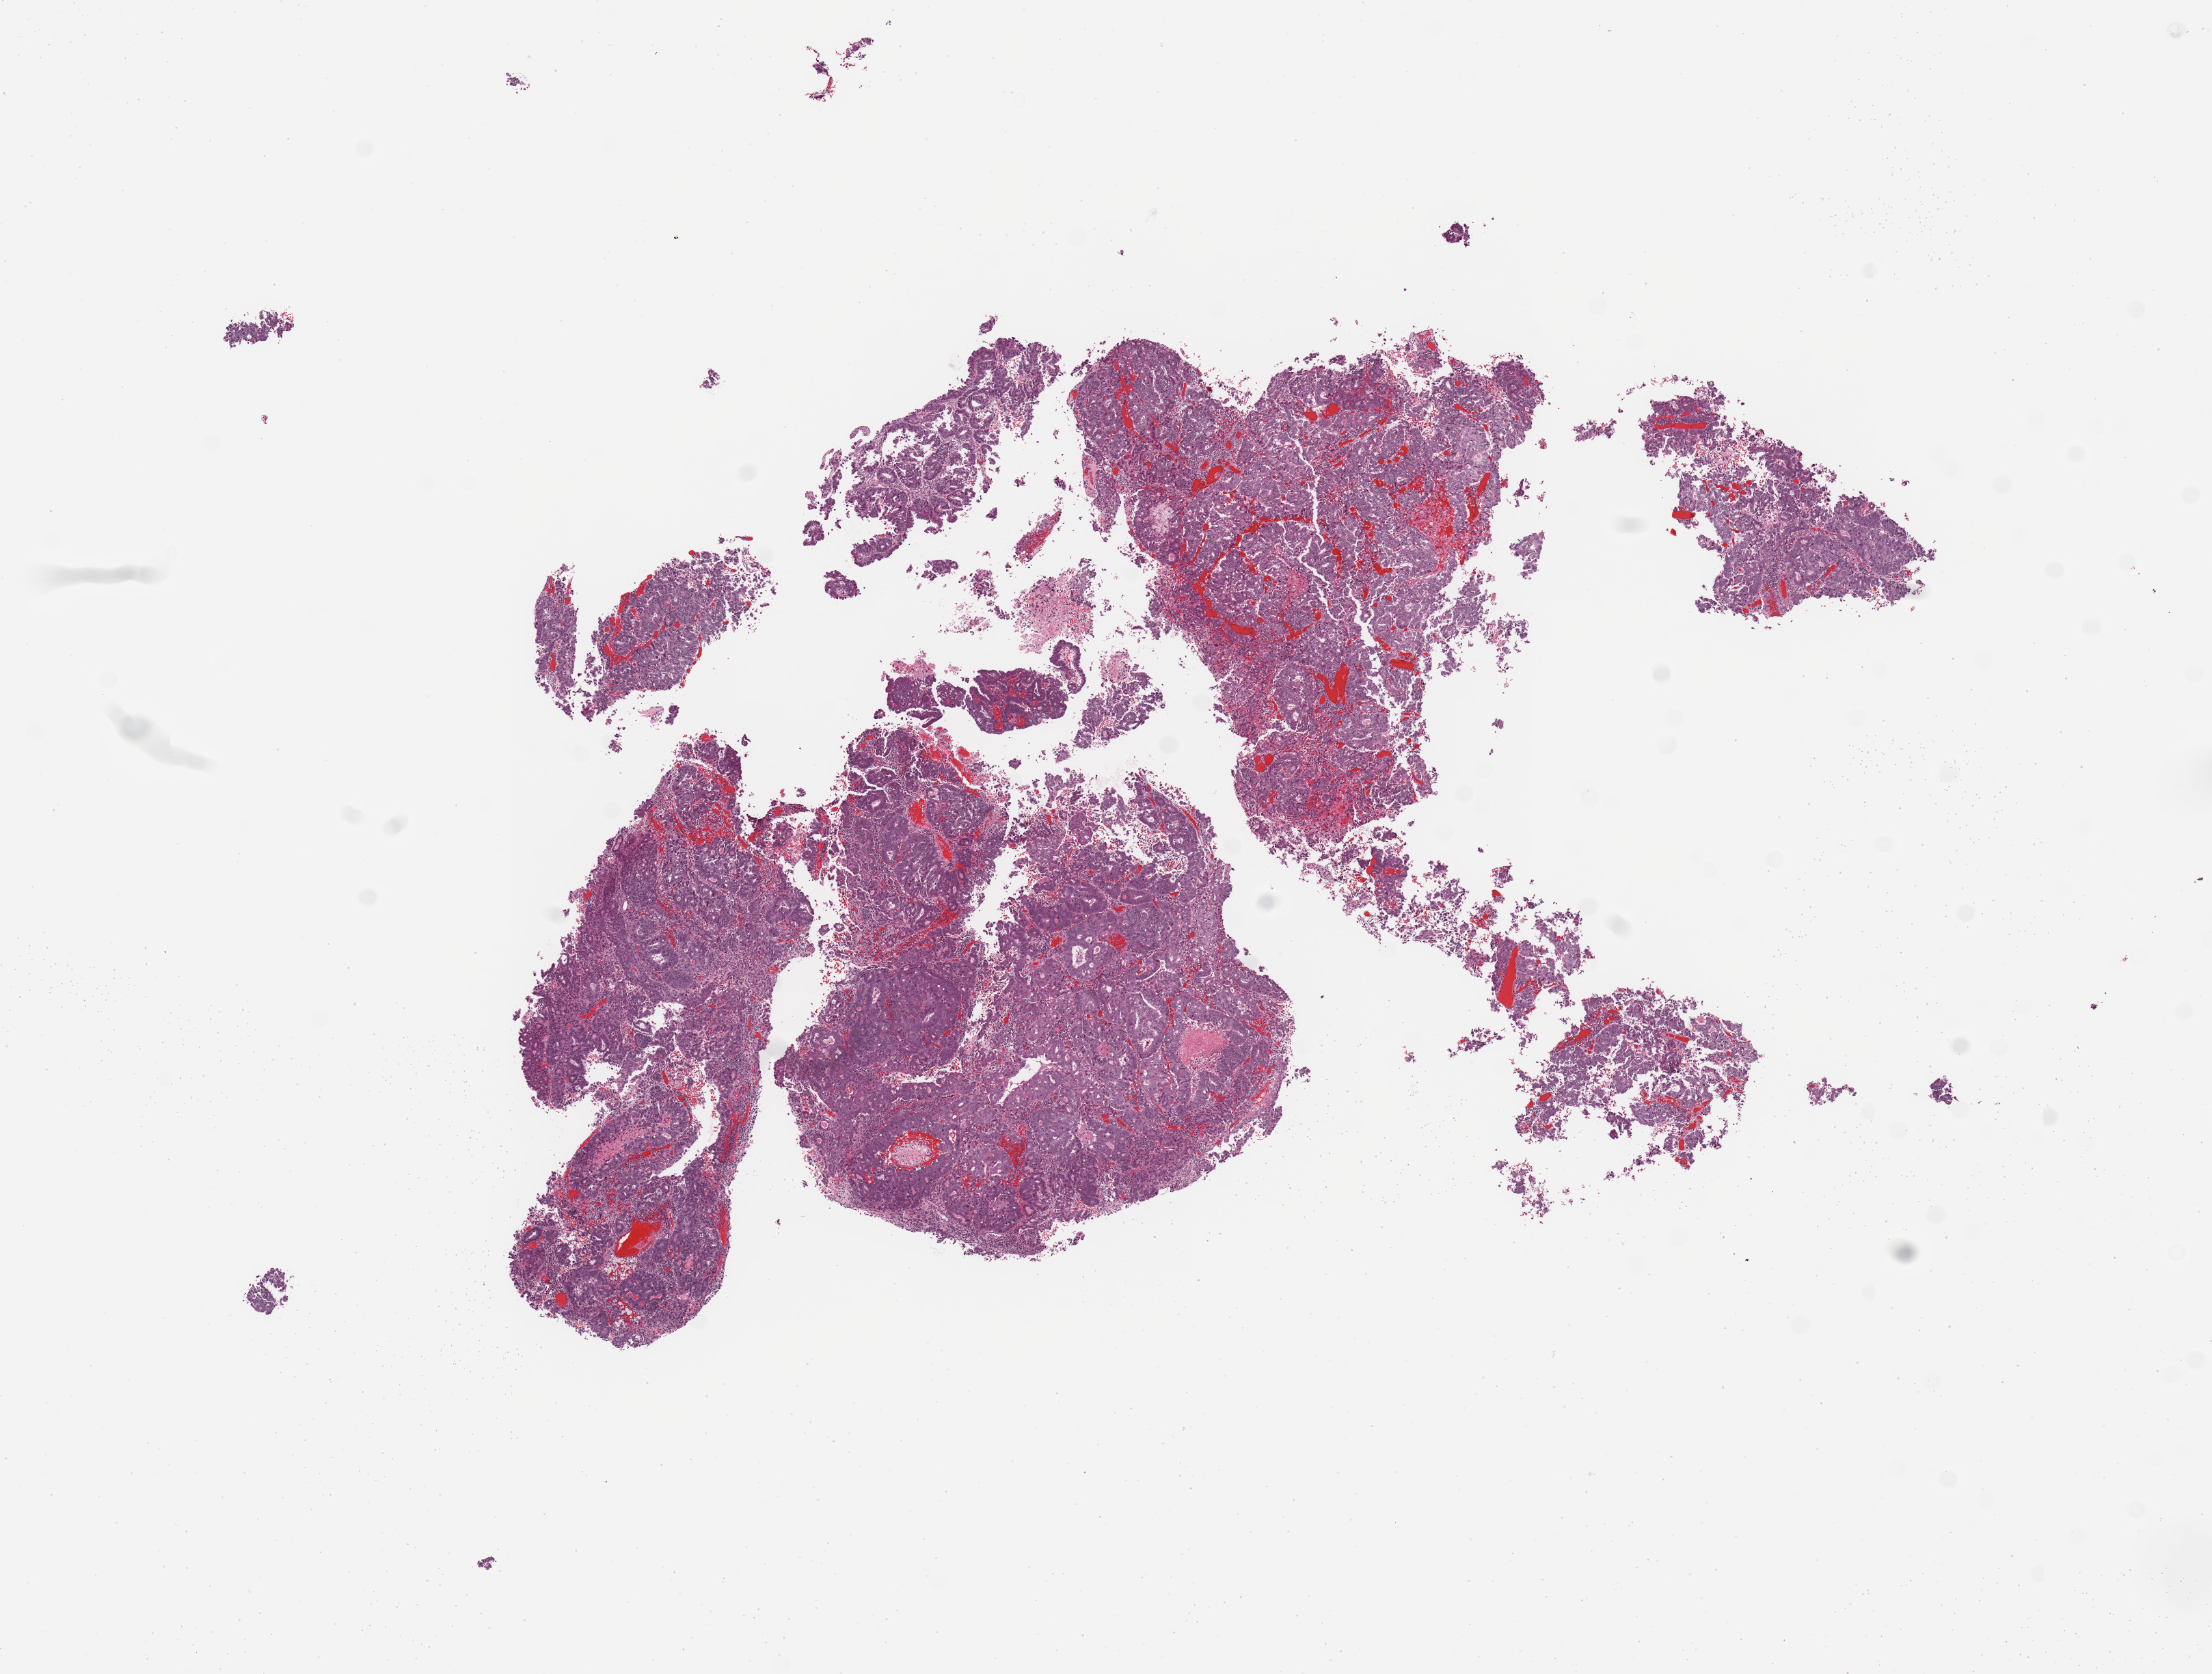
H&E whole-slide image — shown as a low-resolution overview of the whole scanned area (about 12.8 x 9.7 mm, acquisition: 20x scan), uterus, tissue type not recorded.
* patient diagnosis (cohort enrolment): corpus endometrial carcinoma (uterus)